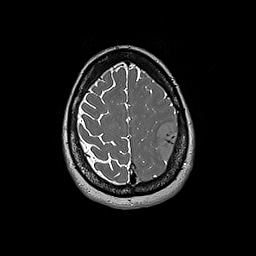
Brain MRI from a brain-tumour surgery series, one axial slice; slice 54 of 192 in the series (ordered by position); 256 × 256 image matrix, field of view 250 × 250 mm. From the clinical record (not read from this slice): histopathology: Glioblastoma; WHO grade: 4; IDH mutation: no; tumour location: Left Frontal.
Annotated regions visible in this slice (outlined manually by an expert reader):
- tumour: bounding box [x1, y1, x2, y2] px = [155, 123, 182, 163]